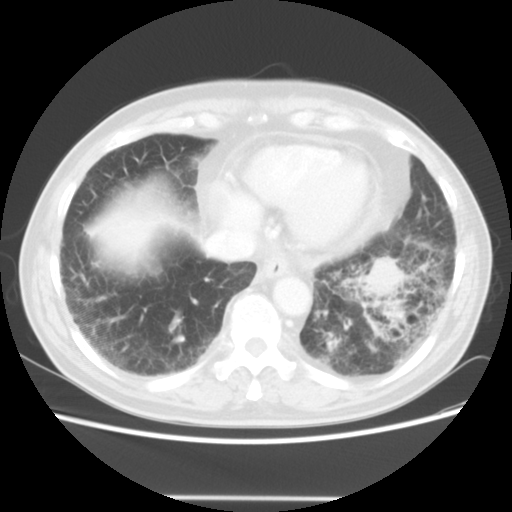
Chest CT, one axial slice; position 12 of 56 along the scan axis; reconstruction kernel STANDARD; lung window (W 1500 / L -600 HU); 5 mm slice thickness; 512 × 512 image matrix, field of view 360 × 360 mm. Patient: male, 66 years. Case-level facts recorded for this patient, not image findings: clinical TNM (as recorded): T4 N3 M0; histopathological grade: G3.
Annotated regions visible in this slice (rectangle marked by the reading radiologist):
- lung tumour (recorded histology: small cell carcinoma): bounding box (x1, y1, x2, y2) in pixels: (365, 249, 406, 309)